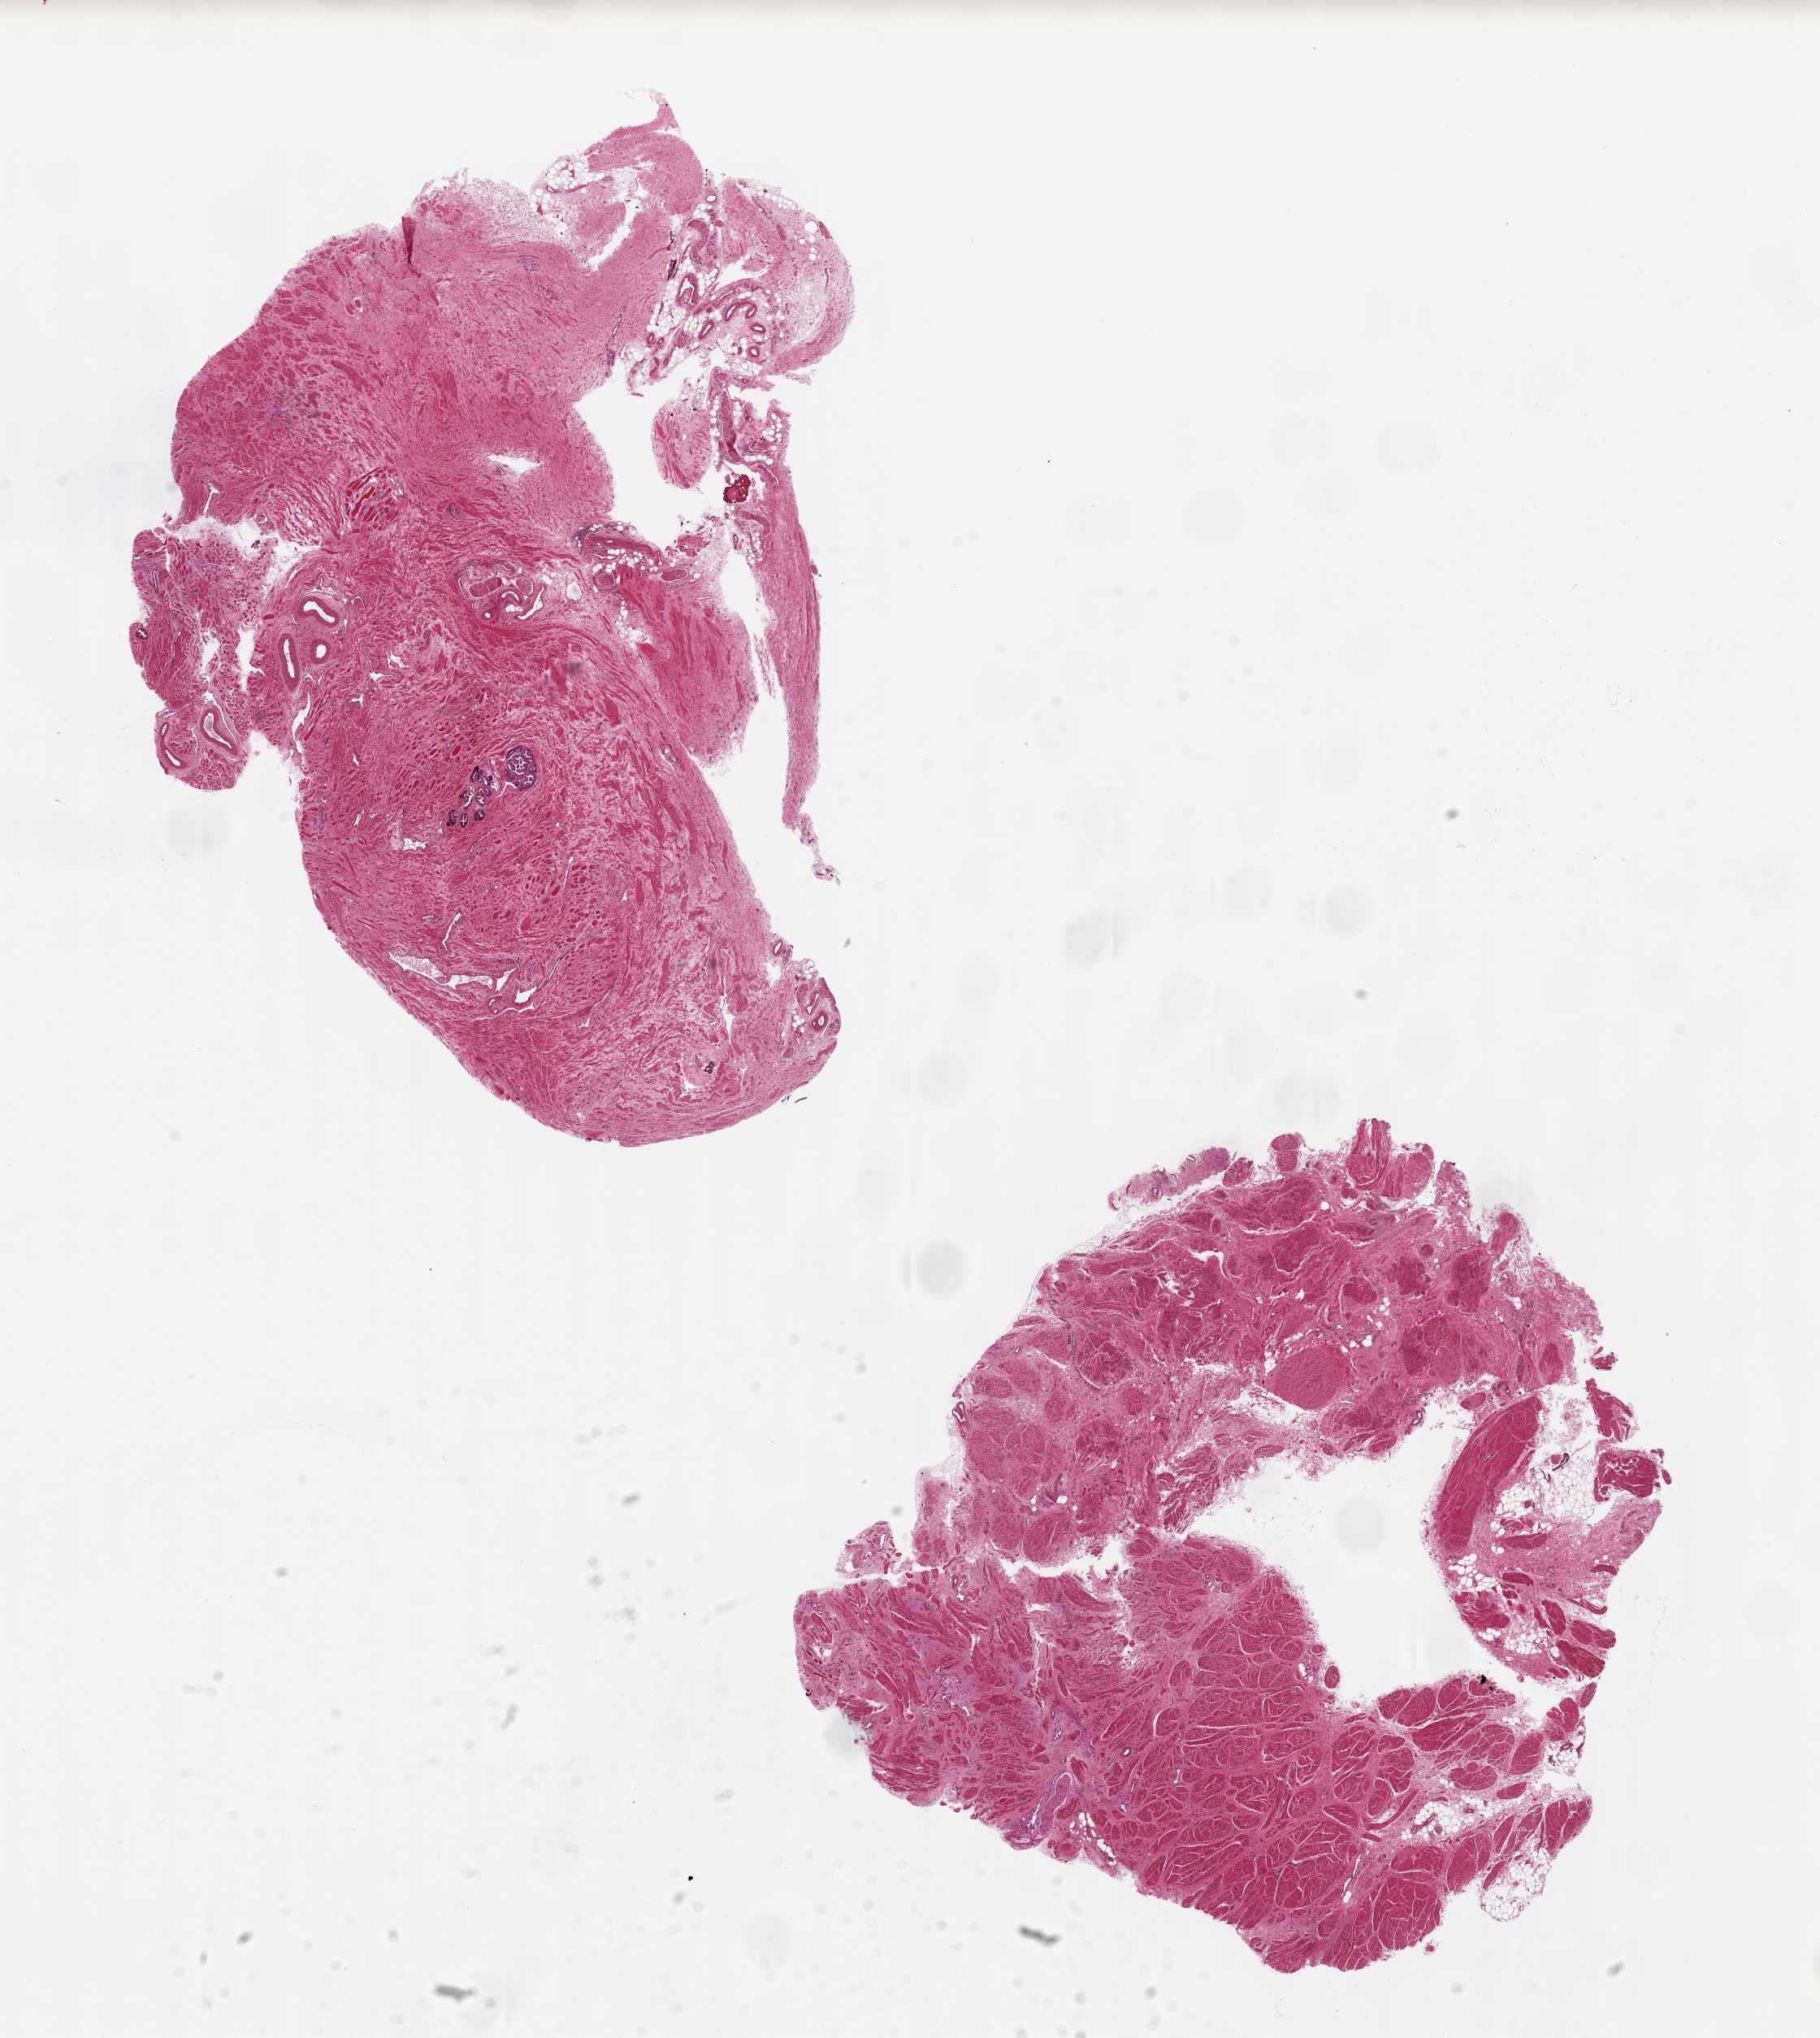
Whole-slide image, H&E stain, shown as a low-resolution overview of the whole scanned area (about 17.7 x 19.8 mm); PAXgene-fixed, paraffin-embedded tissue; section of prostate (target tissue); donor tissue sample. Donor sex: male.
- reviewer comment on this tissue sample: 2 pieces ~9x7mm, mainly fibromuscular stroma, one focal area glandular elements, ~1mm